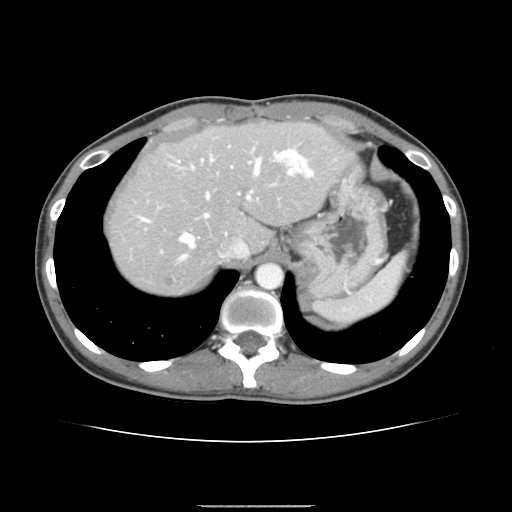
Contrast-enhanced abdominal CT, one axial slice. Slice 116 of 150 in the series (ordered by position). 120 kVp. Intravenous contrast given. Soft-tissue window (W 400 / L 40 HU). 2.5 mm slice thickness. 512 × 512 image matrix, field of view 324 × 324 mm. Female patient, age 32 years. From the clinical record (not read from this slice): diagnosis: colorectal cancer liver metastases, imaged before liver resection; multiple liver metastases: yes; largest metastasis: 0.7 cm; disease in both lobes: no.
Annotated regions visible in this slice (outlined manually by an expert reader):
- hepatic veins: box from (x=140, y=150) to (x=293, y=262) px
- liver: (x=108, y=123)–(x=350, y=295)
- planned liver remnant (the part of the liver to remain after resection): (x=108, y=123)–(x=350, y=261)
- portal vein (with intrahepatic branches): (x=178, y=149)–(x=314, y=218)
- liver metastasis: (x=165, y=277)–(x=174, y=287)